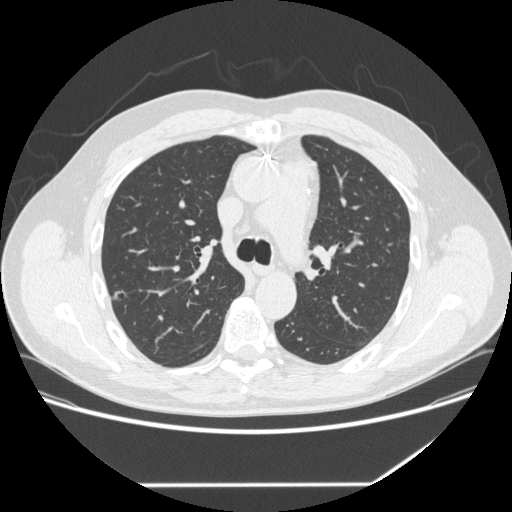
Low-dose screening chest CT, axial slice. First (baseline) screen. Lung window (W 1500 / L -600 HU). 1.25 mm slice thickness. Slice 93 of 262 in the series. Male, age 62 years at enrolment. Current smoker at enrolment.
• Expert-annotated lung lesion, bounding box (x1, y1, x2, y2) in pixels: (99, 281, 132, 310).
• Screening reader's record for this exam: no non-calcified nodule ≥4 mm recorded.
• Participant outcome: lung cancer diagnosed 839 days after this screen — adenocarcinoma, NOS, right upper lobe, moderately differentiated (G2), stage IA (AJCC 6th edition), 12 mm at pathology.